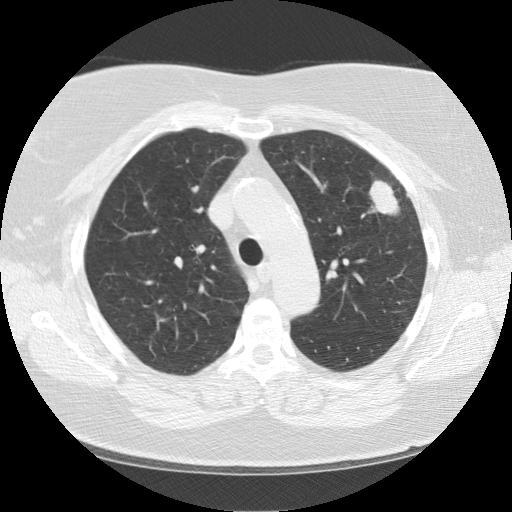
Chest CT (low-dose screening protocol), one axial image; baseline annual screen; lung window (W 1500 / L -600 HU); 2.5 mm slice thickness; standard (soft-tissue) reconstruction kernel (STANDARD); 120 kVp. Female, age 67 years at enrolment. Former smoker at enrolment.
Expert-annotated lung lesion, box from (x=347, y=158) to (x=421, y=229) px. The exam's reader record, not a measurement of the box and not confirmed to be the same lesion: non-calcified nodule or mass ≥4 mm, left upper lobe, 28 × 19 mm, soft tissue attenuation.